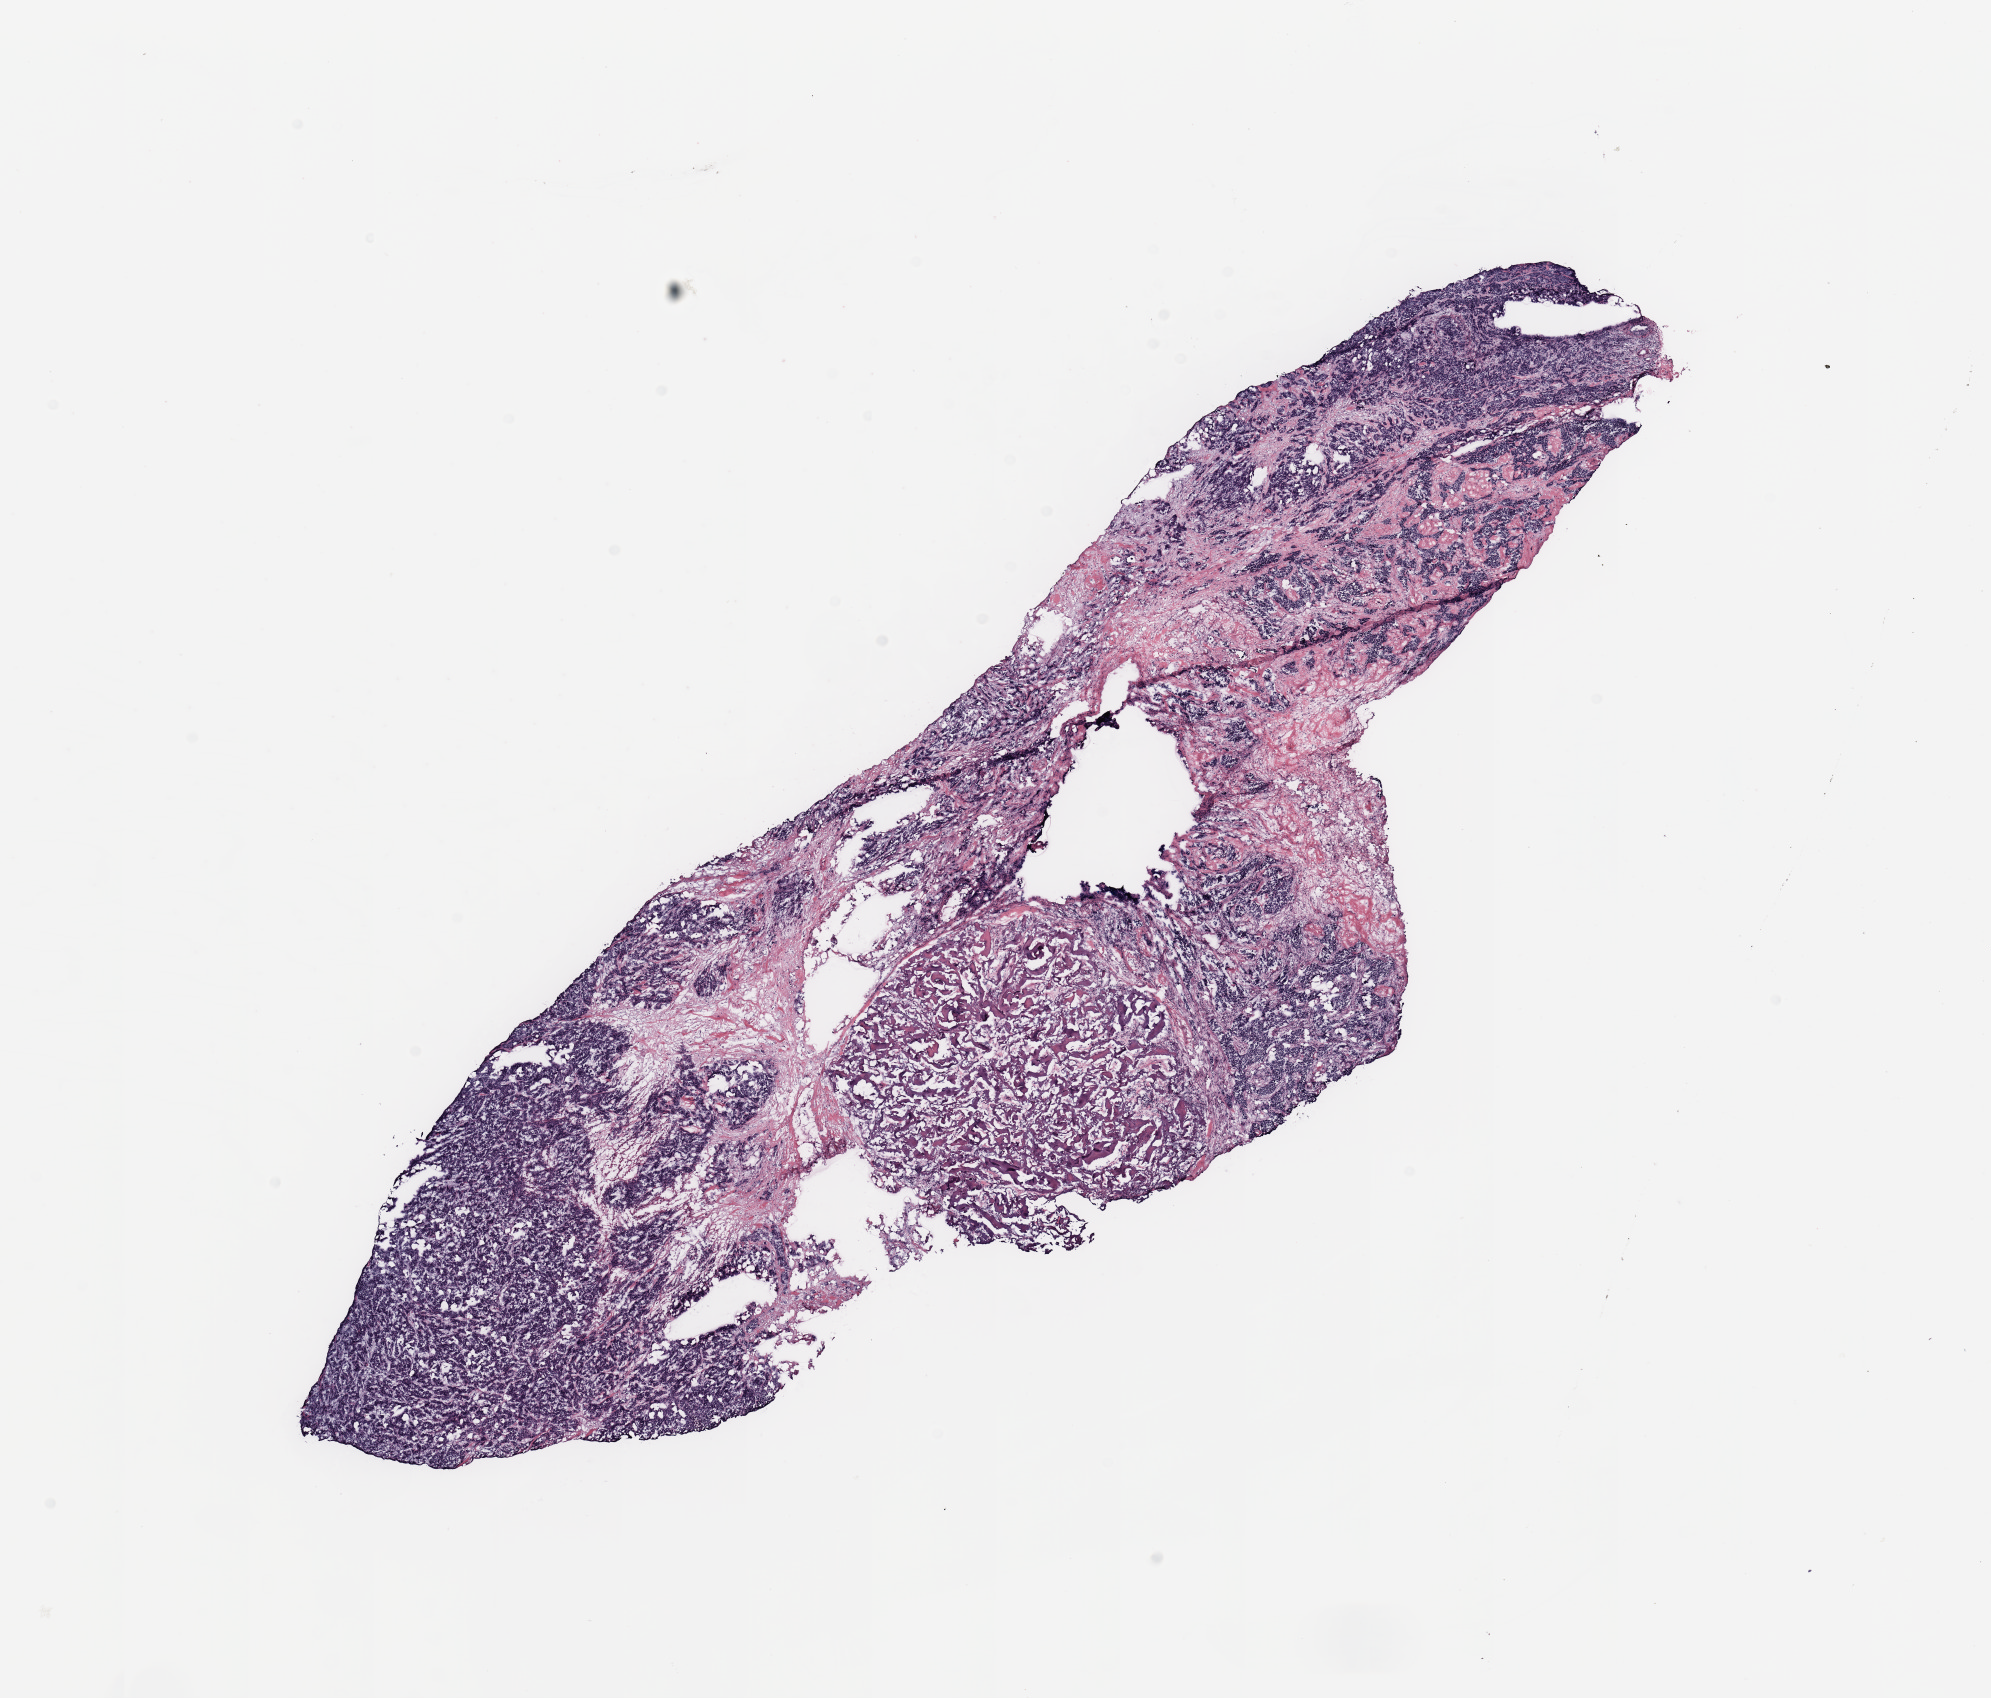
H&E-stained whole-slide image — low-resolution overview of the scanned area, about 15.8 x 13.4 mm; tumour tissue sample, breast. Patient: female, age 60 years.
• diagnosis: Infiltrating duct carcinoma, NOS
• AJCC pathologic stage: IIA